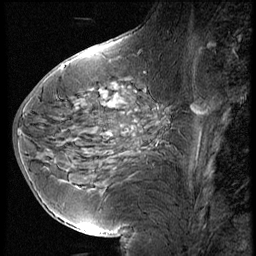
Breast MRI (dynamic contrast-enhanced), one sagittal slice; slice 25 of 60 in the series (ordered by position); 3 images stored at this slice position (order not interpretable as contrast timing); 1.5 T; TE 4.2 ms, TR 9 ms; 2.5 mm slice thickness; 256 × 256 image matrix, field of view 180 × 180 mm. Female patient, age 56 years. From the clinical record (not read from this slice): setting: breast cancer imaged before/during neoadjuvant chemotherapy.
Structures marked on this image (semi-automatically segmented with operator editing):
- analysis volume of interest (the breast-tissue region the enhancement analysis was run in; not a lesion): bounding box <137,61,218,137> (left, top, right, bottom; pixels)
- tumour enhancement mask (voxels above the 140 % enhancement threshold inside the analysis volume of interest): <192,104,201,113>